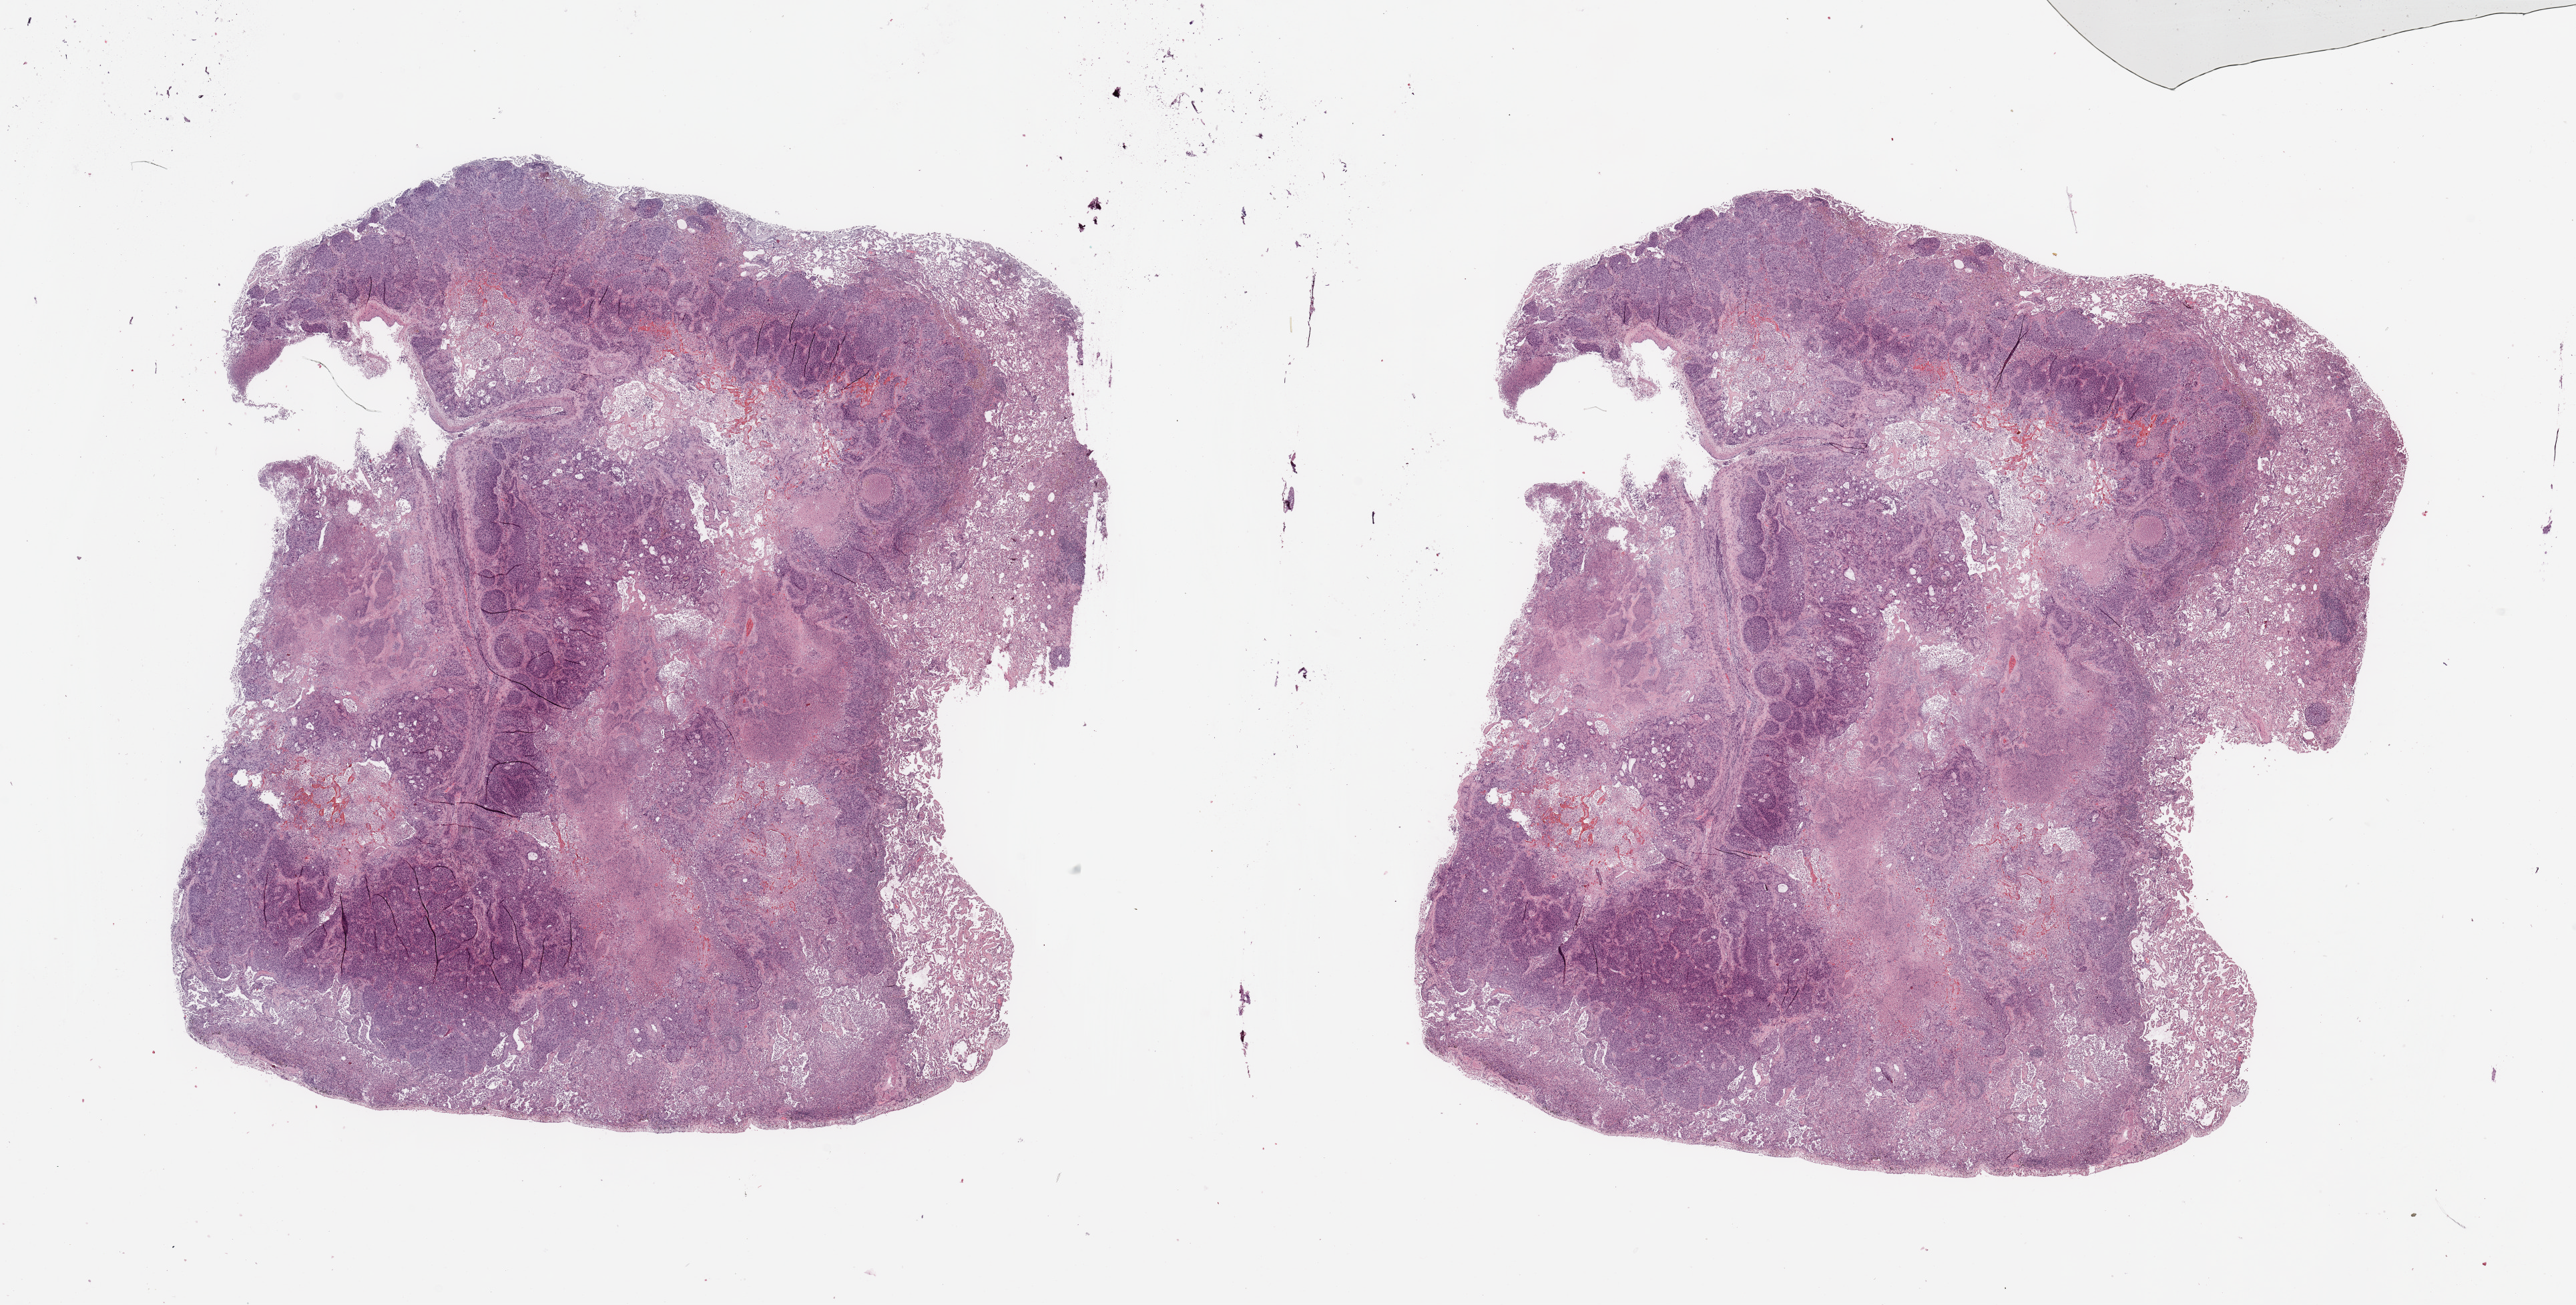
H&E-stained whole-slide image, a low-resolution overview of the entire scanned area, about 30.5 x 15.5 mm (acquisition: 20x scan). Tumour tissue sample, lung. 57-year-old male patient. Histologic grade: G3 (poorly differentiated).
* AJCC pathologic stage: IA
* primary tumour site (as recorded): right lower lobe
* histologic diagnosis: Squamous cell carcinoma, NOS